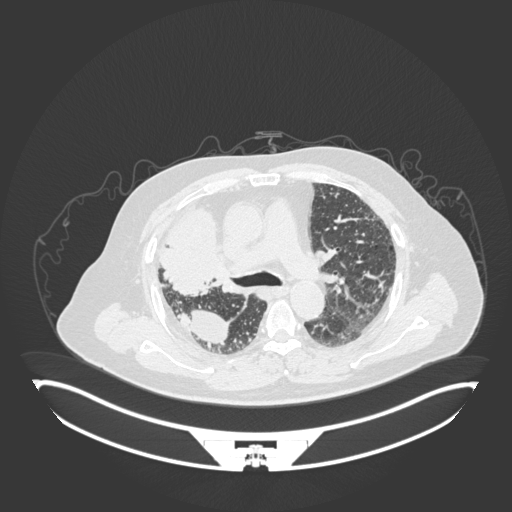
Chest CT, one axial slice. Slice 114 of 201 in the series (ordered by position). Reconstruction kernel B30f. 120 kVp. Lung window (W 1500 / L -600 HU). 1 mm slice thickness. 512 × 512 image matrix, field of view 500 × 500 mm. Patient: male, 69 years. From the clinical record (not read from this slice): clinical TNM (as recorded): T4 N3 M1.
Annotated regions visible in this slice (bounding box drawn by a radiologist):
- lung tumour (recorded histology: adenocarcinoma): bounding box [x1, y1, x2, y2] px = [148, 203, 232, 295]